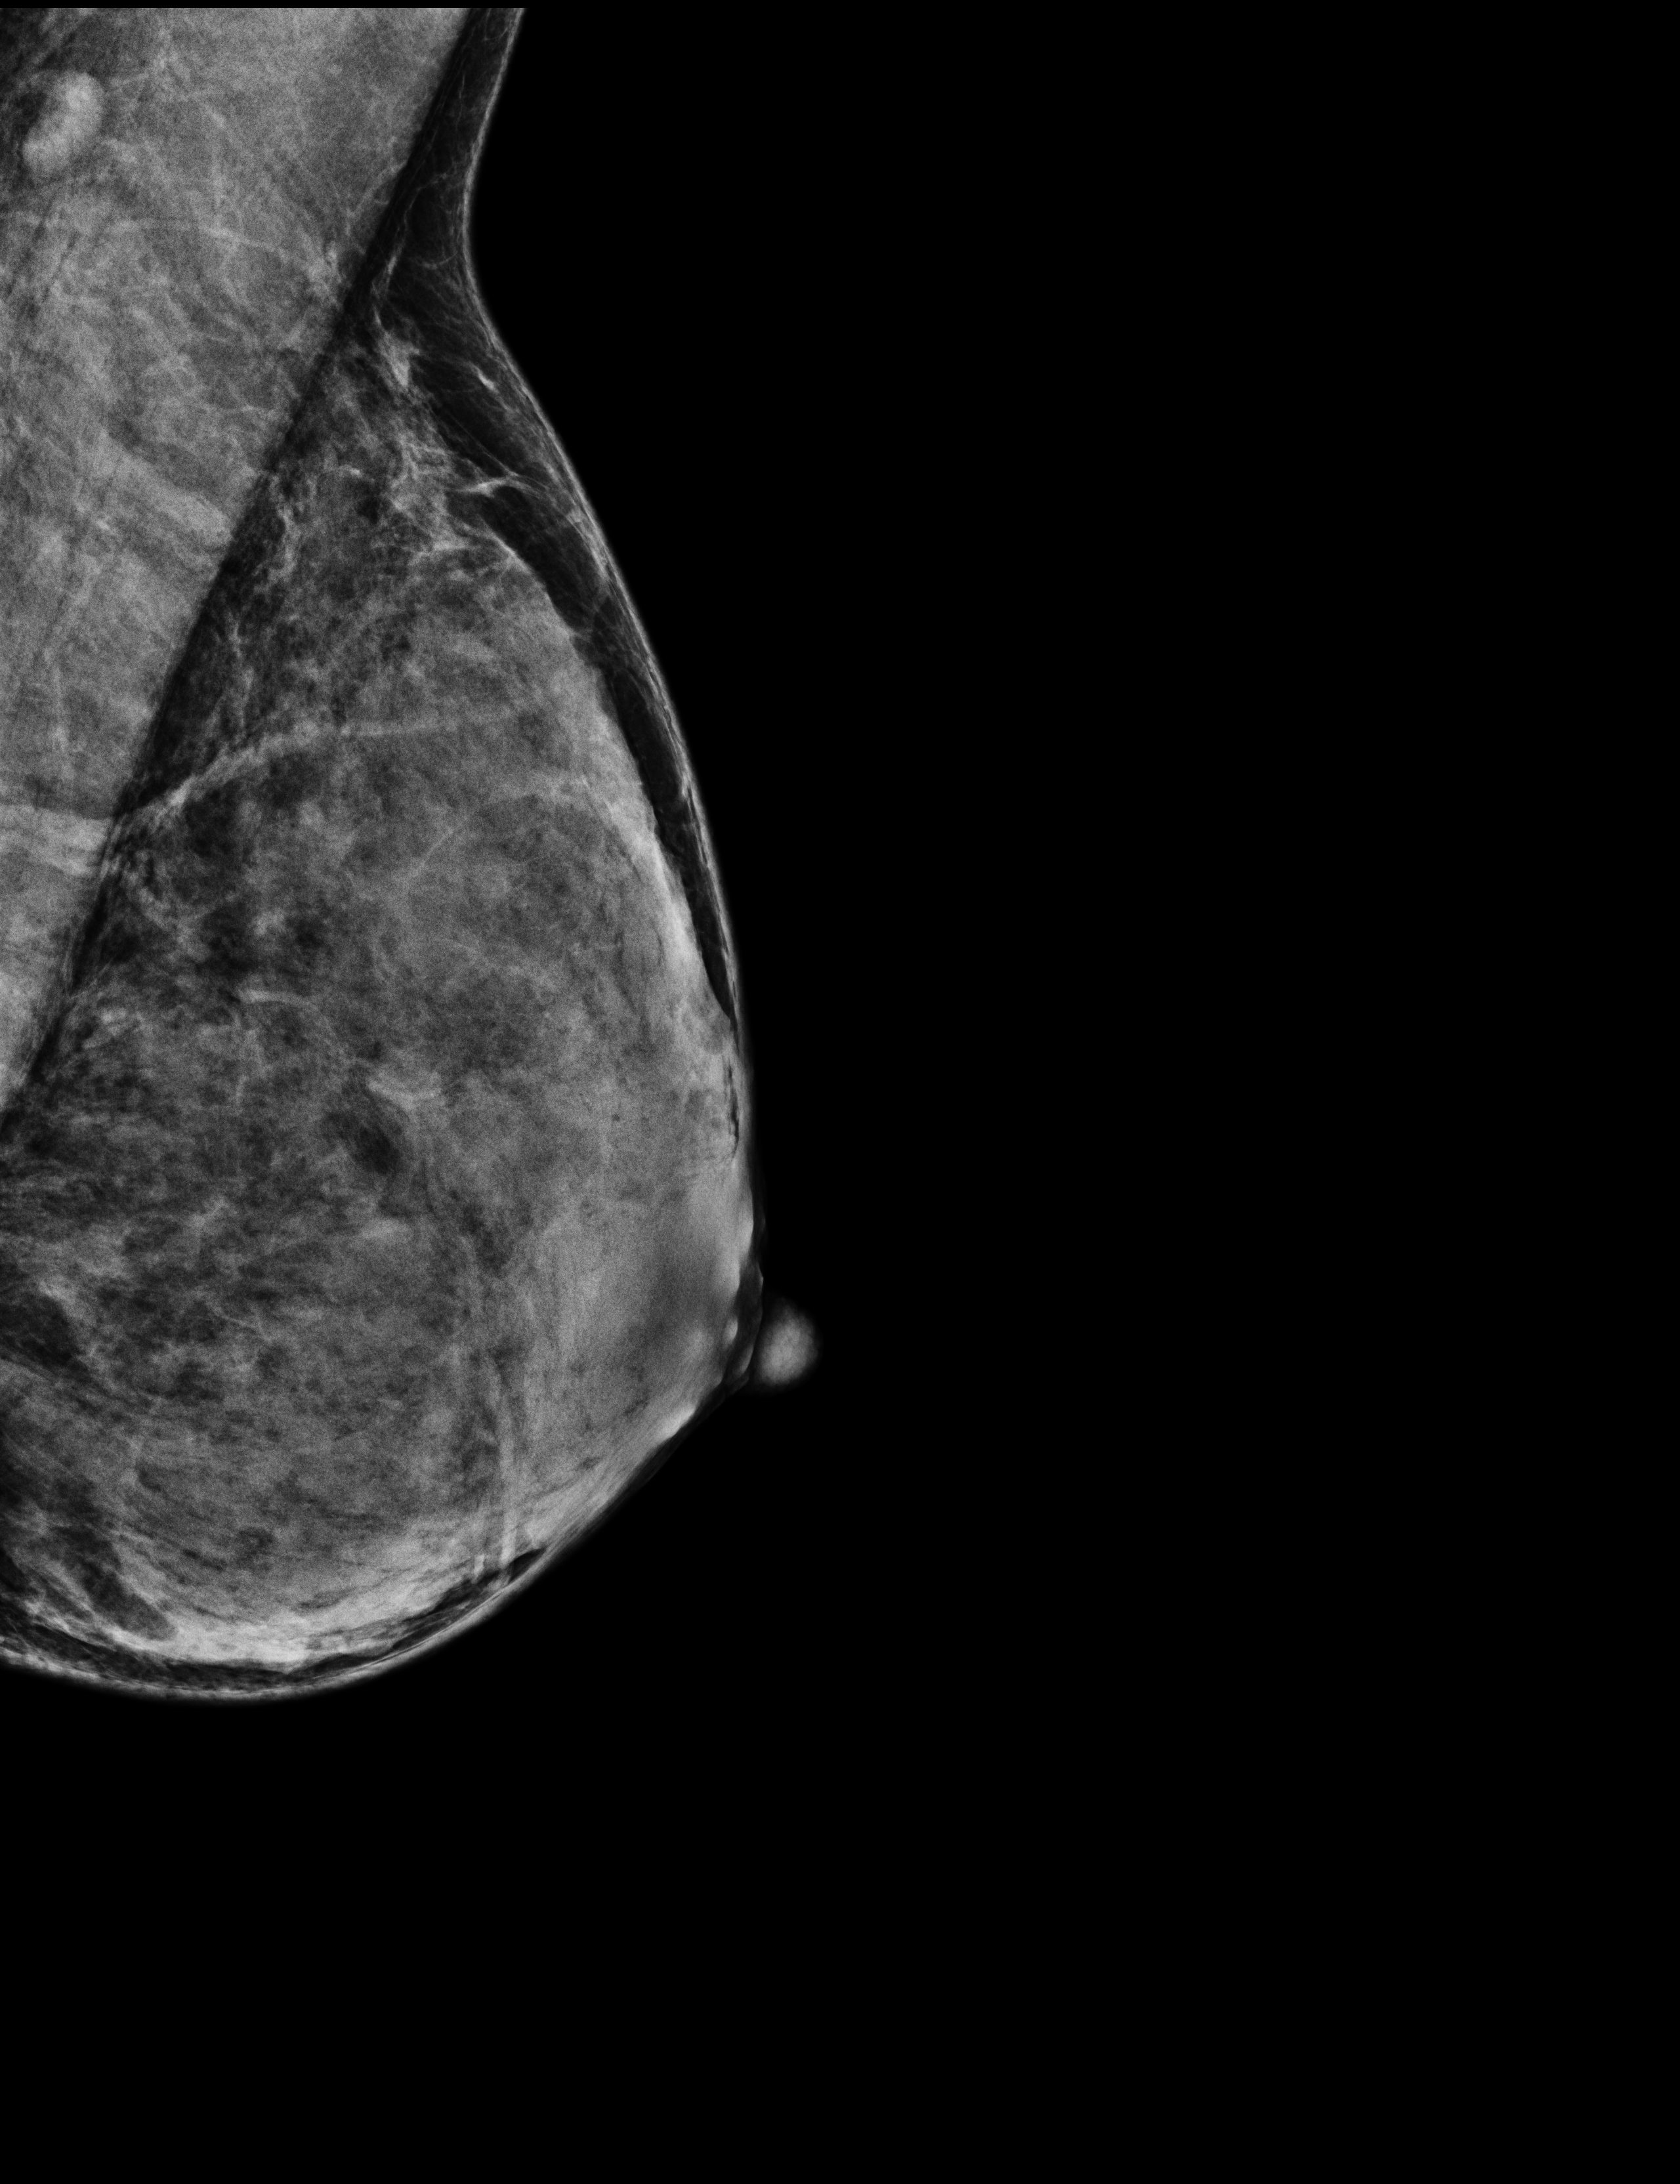
Screening examination.
Image type: full-field digital mammogram. Breast: left. Projection: mediolateral oblique (MLO) view.